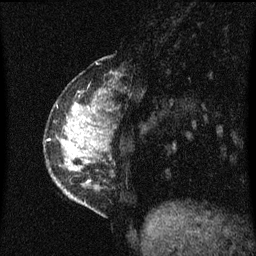
Breast MRI (dynamic contrast-enhanced), one sagittal slice. Position 16 of 60 along the scan axis. Dynamic contrast-enhanced series, image 2 of 3 at this slice position (ordered by acquisition). 1.5 T. TE 4.2 ms, TR 8.4 ms. 2 mm slice thickness. 256 × 256 image matrix, field of view 200 × 200 mm. Patient: female, 34 years. From the clinical record (not read from this slice): setting: breast cancer imaged before/during neoadjuvant chemotherapy; receptor status: HR-positive, HER2-negative.
Annotated regions visible in this slice (semi-automatic segmentation, software-assisted and operator-edited):
- analysis volume of interest (the breast-tissue region the enhancement analysis was run in; not a lesion): bounding box <56,100,109,207> (left, top, right, bottom; pixels)
- tumour enhancement mask (voxels above the 70 % enhancement threshold inside the analysis volume of interest): <76,126,81,155>